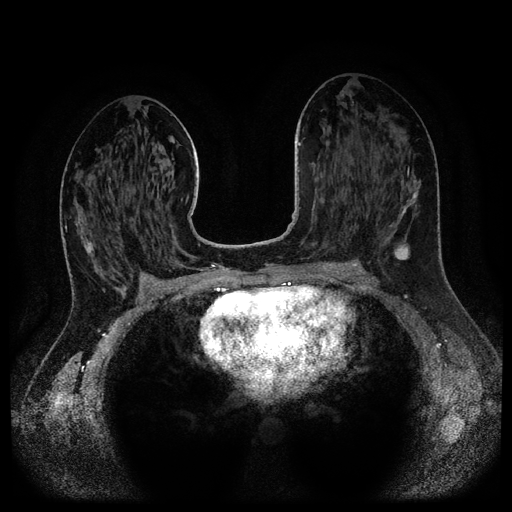
Breast MRI (dynamic contrast-enhanced, multi-phase), one axial slice; slice 58 of 116 in the series (ordered by position); dynamic contrast-enhanced series, time point 2 of 5 at this slice position (early post-contrast); 1.5 T; TE 2.6 ms, TR 5.3 ms; 2.1 mm slice thickness; 512 × 512 image matrix. Patient: female, 37 years.
Outlined on this slice (semi-automatic segmentation, software-assisted and operator-edited):
- breast lesion (labelled 'tumour' in the annotation; benign lesions carry a separate 'benign' label): bounding box (x1, y1, x2, y2) in pixels: (383, 193, 417, 260)